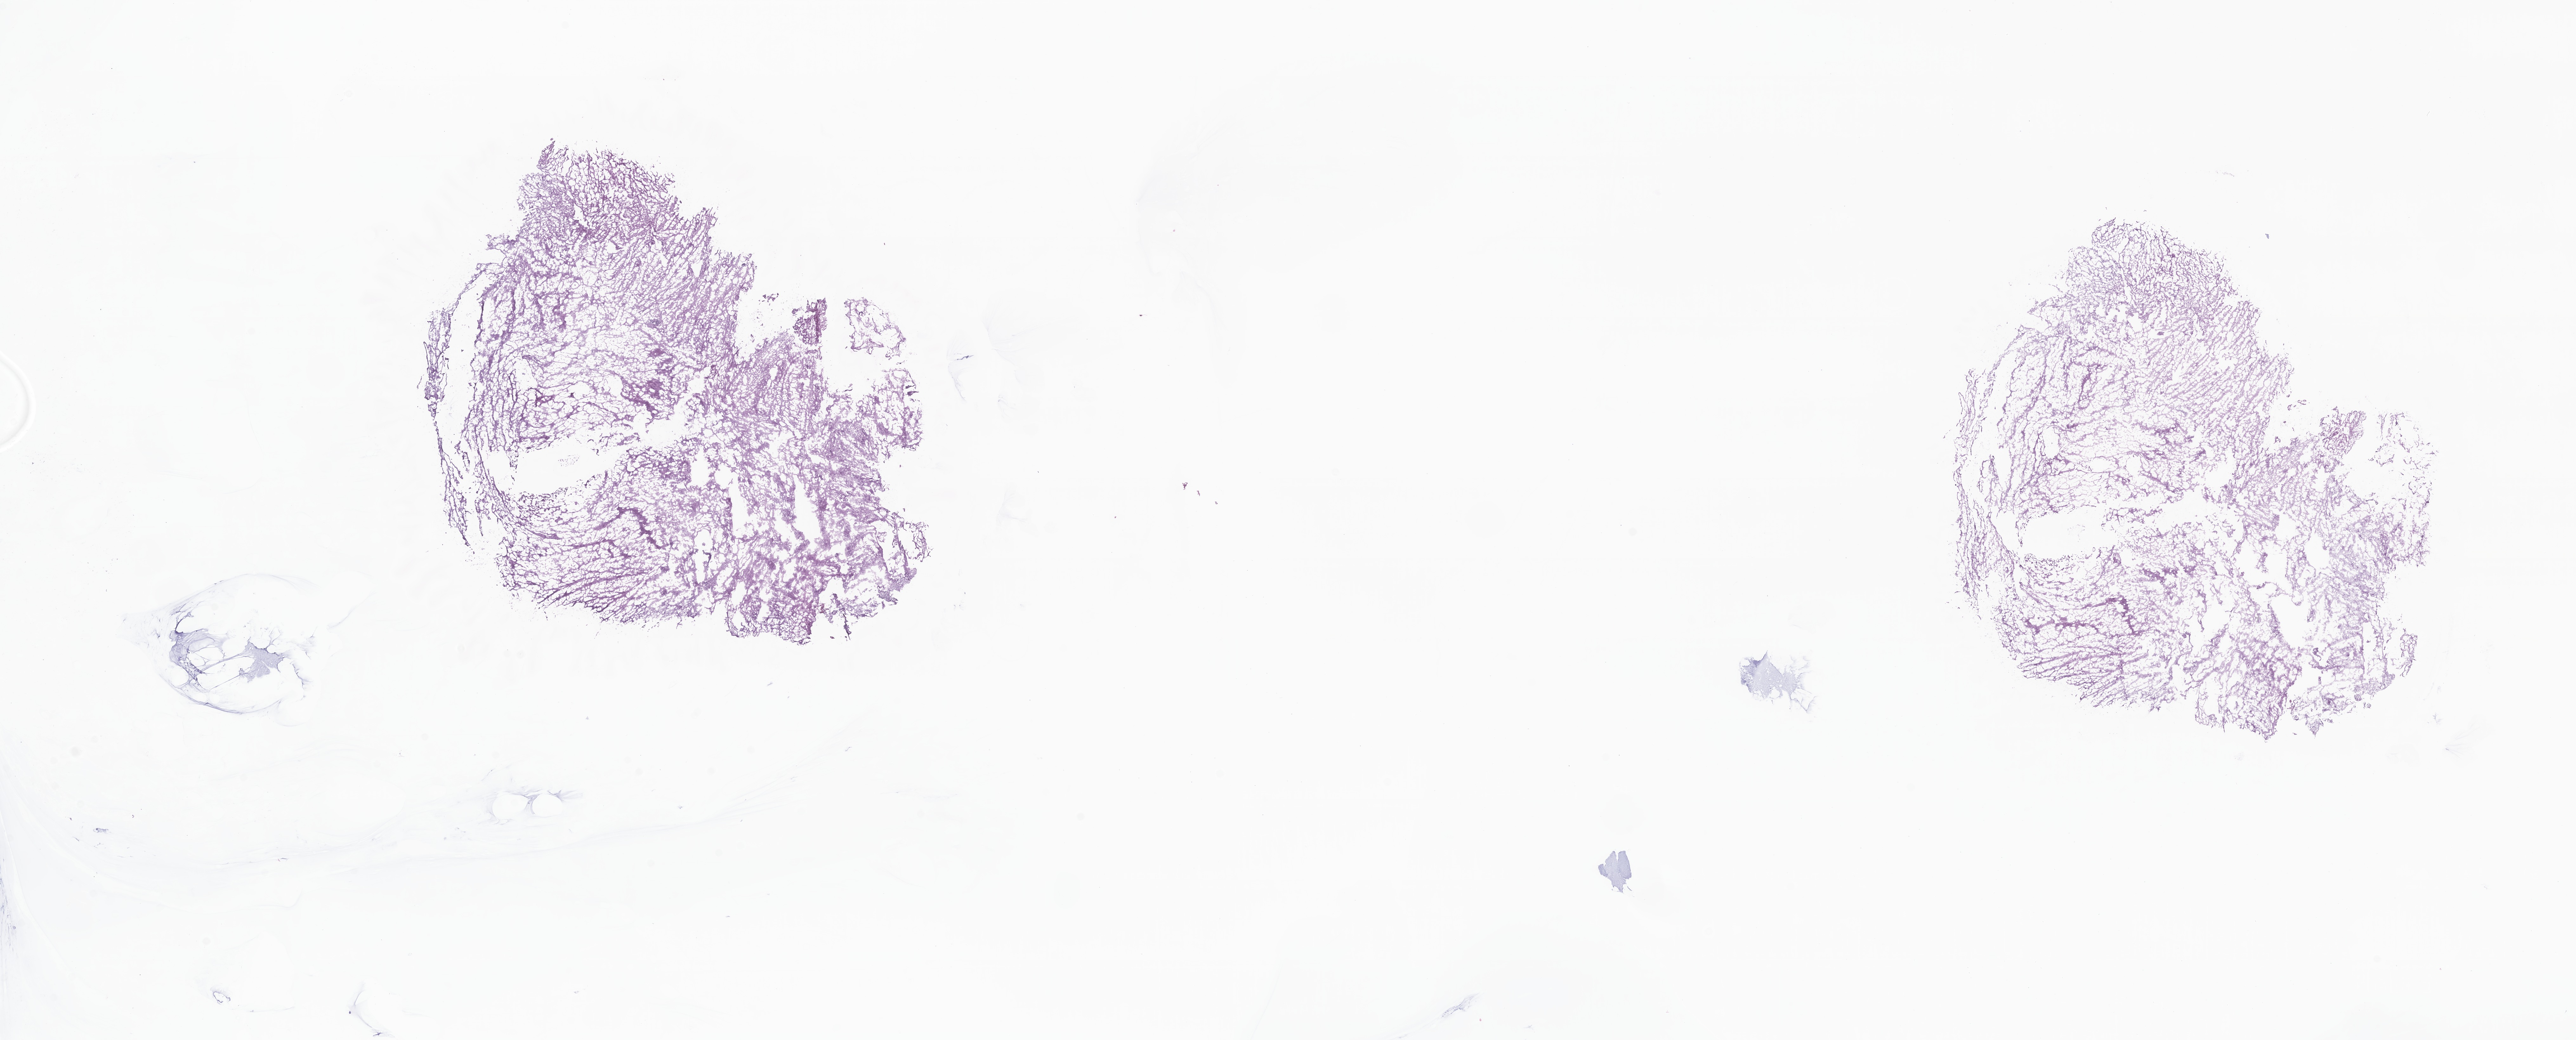
Digitized hematoxylin and eosin (H&E)-stained section of tumor tissue from the brain, whole scanned area (about 34.2 x 13.8 mm) shown as a low-resolution overview. Cryosection (OCT / tissue freezing medium). Male patient, age 40 months (3 years 4 months).
Diagnosis: Glioma, malignant.